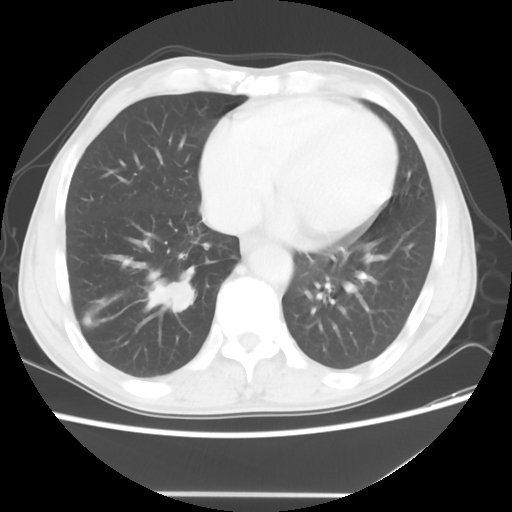
Chest CT, one axial slice. Slice 17 of 56 in the series (ordered by position). Lung window (W 1500 / L -600 HU). 5 mm slice thickness. 512 × 512 image matrix. Male patient, age 65 years. Case-level facts recorded for this patient, not image findings: clinical TNM (as recorded): T1c N3 M0.
Annotated regions visible in this slice (rectangle marked by the reading radiologist):
- lung tumour (recorded histology: small cell carcinoma): bounding box (x1, y1, x2, y2) in pixels: (142, 272, 203, 315)